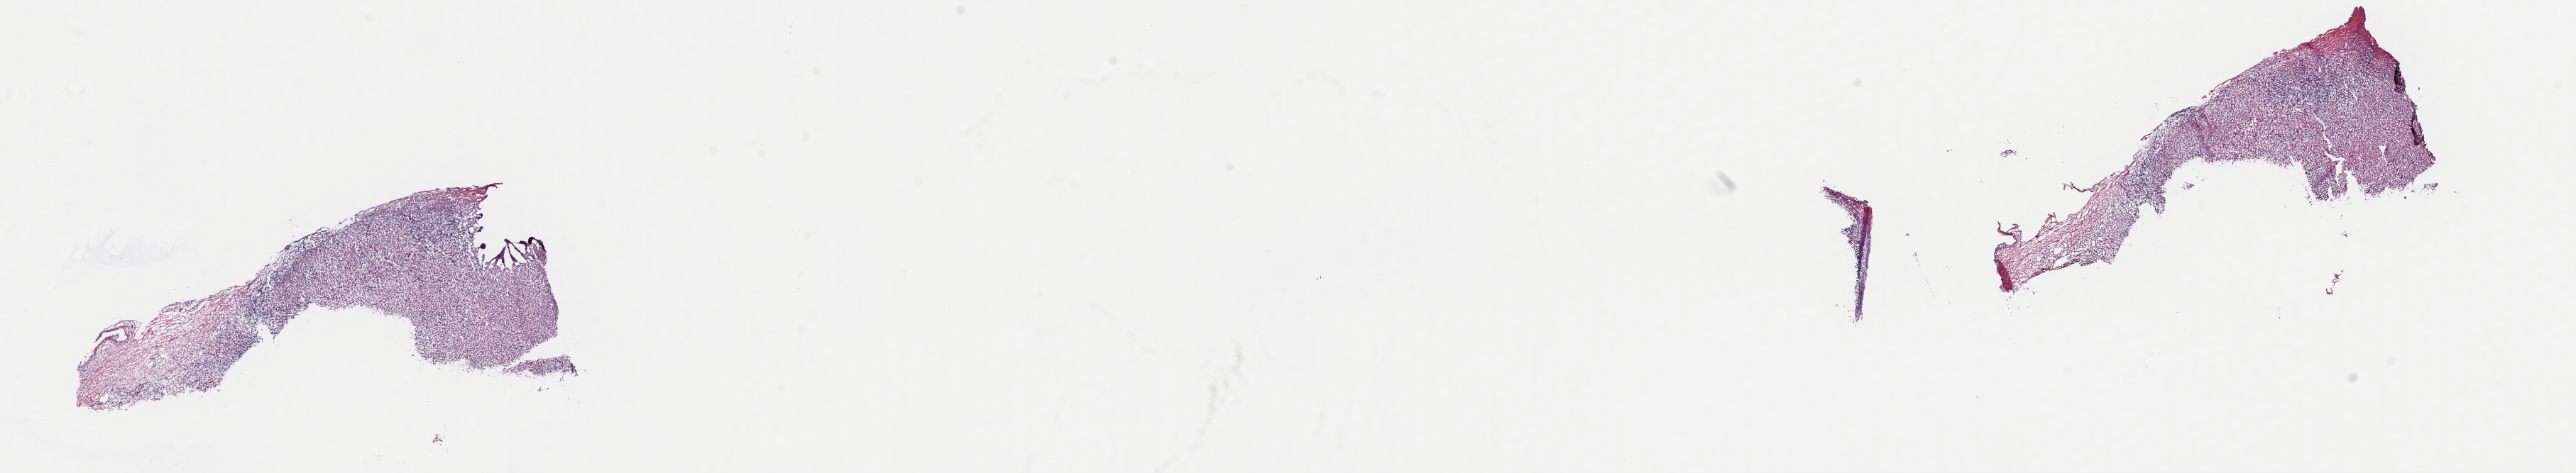
Whole-slide histology image, Hematoxylin and eosin (H&E) stained — a low-resolution overview of the entire scanned area, about 28.7 x 5.3 mm (acquisition: 40x scan); frozen section from the top of the tissue portion; primary tumour sample from the mesothelium. Male, age 78 years at initial diagnosis. Slide review estimates, as recorded: tumour cells 80%, tumour nuclei 80%, normal cells 0%, stromal cells 5%, necrosis 15%. Infiltration values recorded for this section: lymphocyte infiltration 40%, monocyte infiltration 20%, neutrophil infiltration 20%.
AJCC pathologic stage: II (6th edition). Histologic diagnosis: Mesothelioma, biphasic, malignant (pleura, NOS).